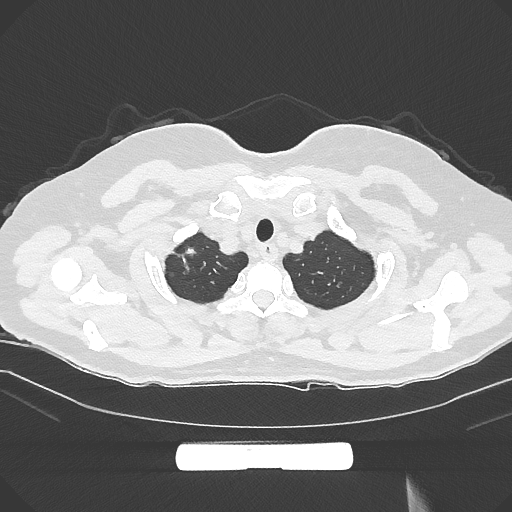
Chest CT, one axial slice. Slice 266 of 294 in the series (ordered by position). Reconstruction kernel IMR1,SharpPlus. 120 kVp. Lung window (W 1500 / L -600 HU). 512 × 512 image matrix, field of view 369 × 369 mm. Female patient, age 58 years. Case-level facts recorded for this patient, not image findings: clinical TNM (as recorded): T1b N0 M0.
Annotated regions visible in this slice (bounding box drawn by a radiologist):
- lung tumour (recorded histology: adenocarcinoma): bounding box (x1, y1, x2, y2) in pixels: (171, 242, 213, 283)